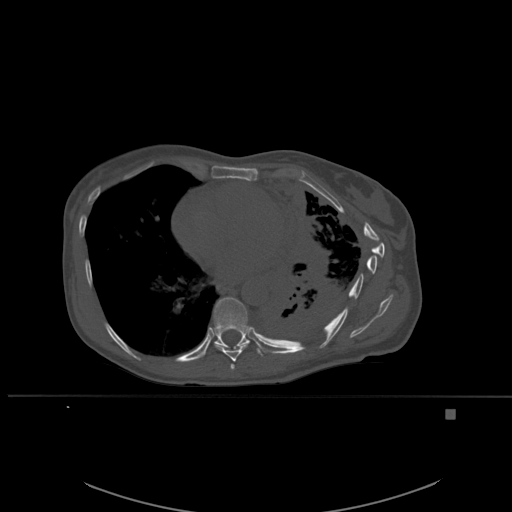
CT including the spine, one axial slice. Position 343 of 537 along the scan axis. Bone window (W 1800 / L 400 HU). 1.5 mm slice thickness. 512 × 512 image matrix. Female patient, age 45 years. Case-level facts recorded for this patient, not image findings: primary cancer: lung.
Outlined on this slice (semi-automatically segmented with operator editing):
- T7 vertebra: bounding box (x1, y1, x2, y2) in pixels: (230, 364, 235, 370)
- T8 vertebra: (214, 344, 249, 362)
- T9 vertebra: (205, 297, 264, 357)